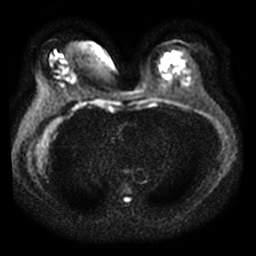
Breast MRI, one axial slice. Position 20 of 40 along the scan axis. Diffusion-weighted series; image 2 of 4 stored at this slice position (different b-values; order by instance number). 3 T. 5 mm slice thickness. 256 × 256 image matrix, field of view 340 × 340 mm. Female patient.
Outlined on this slice (expert manual segmentation):
- tumour on diffusion-weighted imaging: bounding box [x1, y1, x2, y2] px = [60, 54, 62, 57]